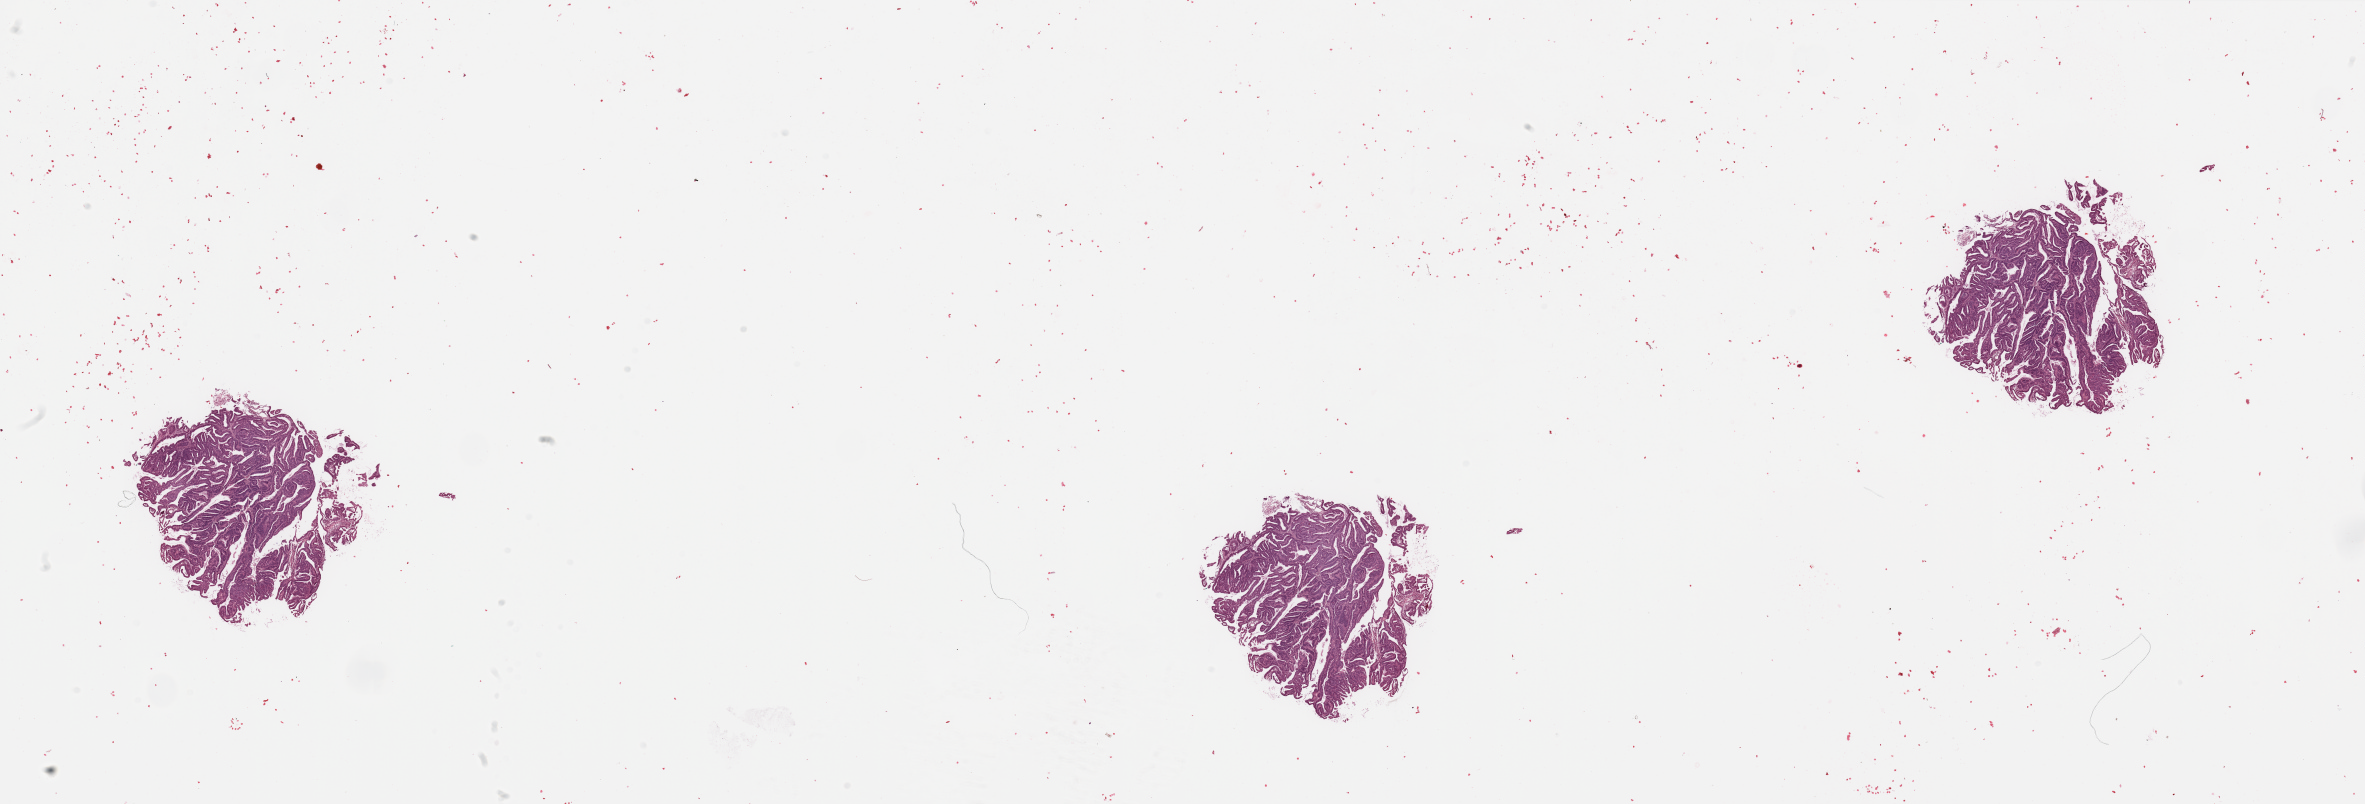
Hematoxylin and eosin (H&E) stained whole-slide image, shown as a low-resolution overview of the whole scanned area (about 37.4 x 12.7 mm); tumour tissue sample, sampled site: uterus. 68-year-old female patient. Histologic grade: G2 (moderately differentiated). Composition of this section per pathologist review: tumour nuclei 90%, necrosis 2%.
Histologic diagnosis: Endometrioid adenocarcinoma, NOS. Primary tumour site (as recorded): anterior endometrium. AJCC pathologic stage: I.